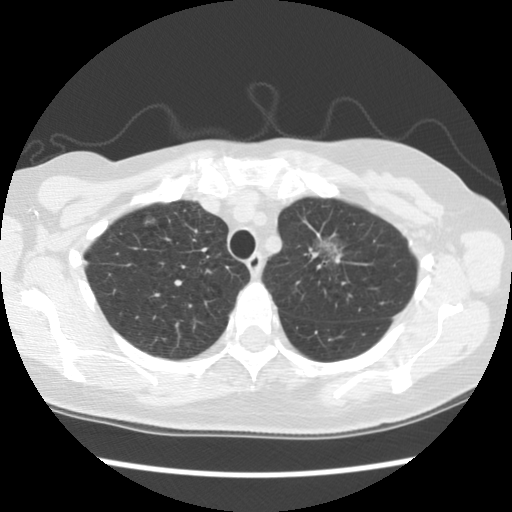
Low-dose screening chest CT, axial slice; second annual screen; lung window (W 1500 / L -600 HU). Female, age 65 years at enrolment. Former smoker at enrolment.
Lesion marked by an expert reader, box from (x=300, y=224) to (x=363, y=285) px. The screening reader recorded 2 non-calcified nodules or masses ≥4 mm on this exam (right upper lobe, left upper lobe); which of them this box marks is not recorded. Participant outcome: lung cancer diagnosed 481 days after this screen — adenocarcinoma, NOS, left upper lobe, moderately differentiated (G2), stage IA (AJCC 6th edition), 30 mm at pathology.